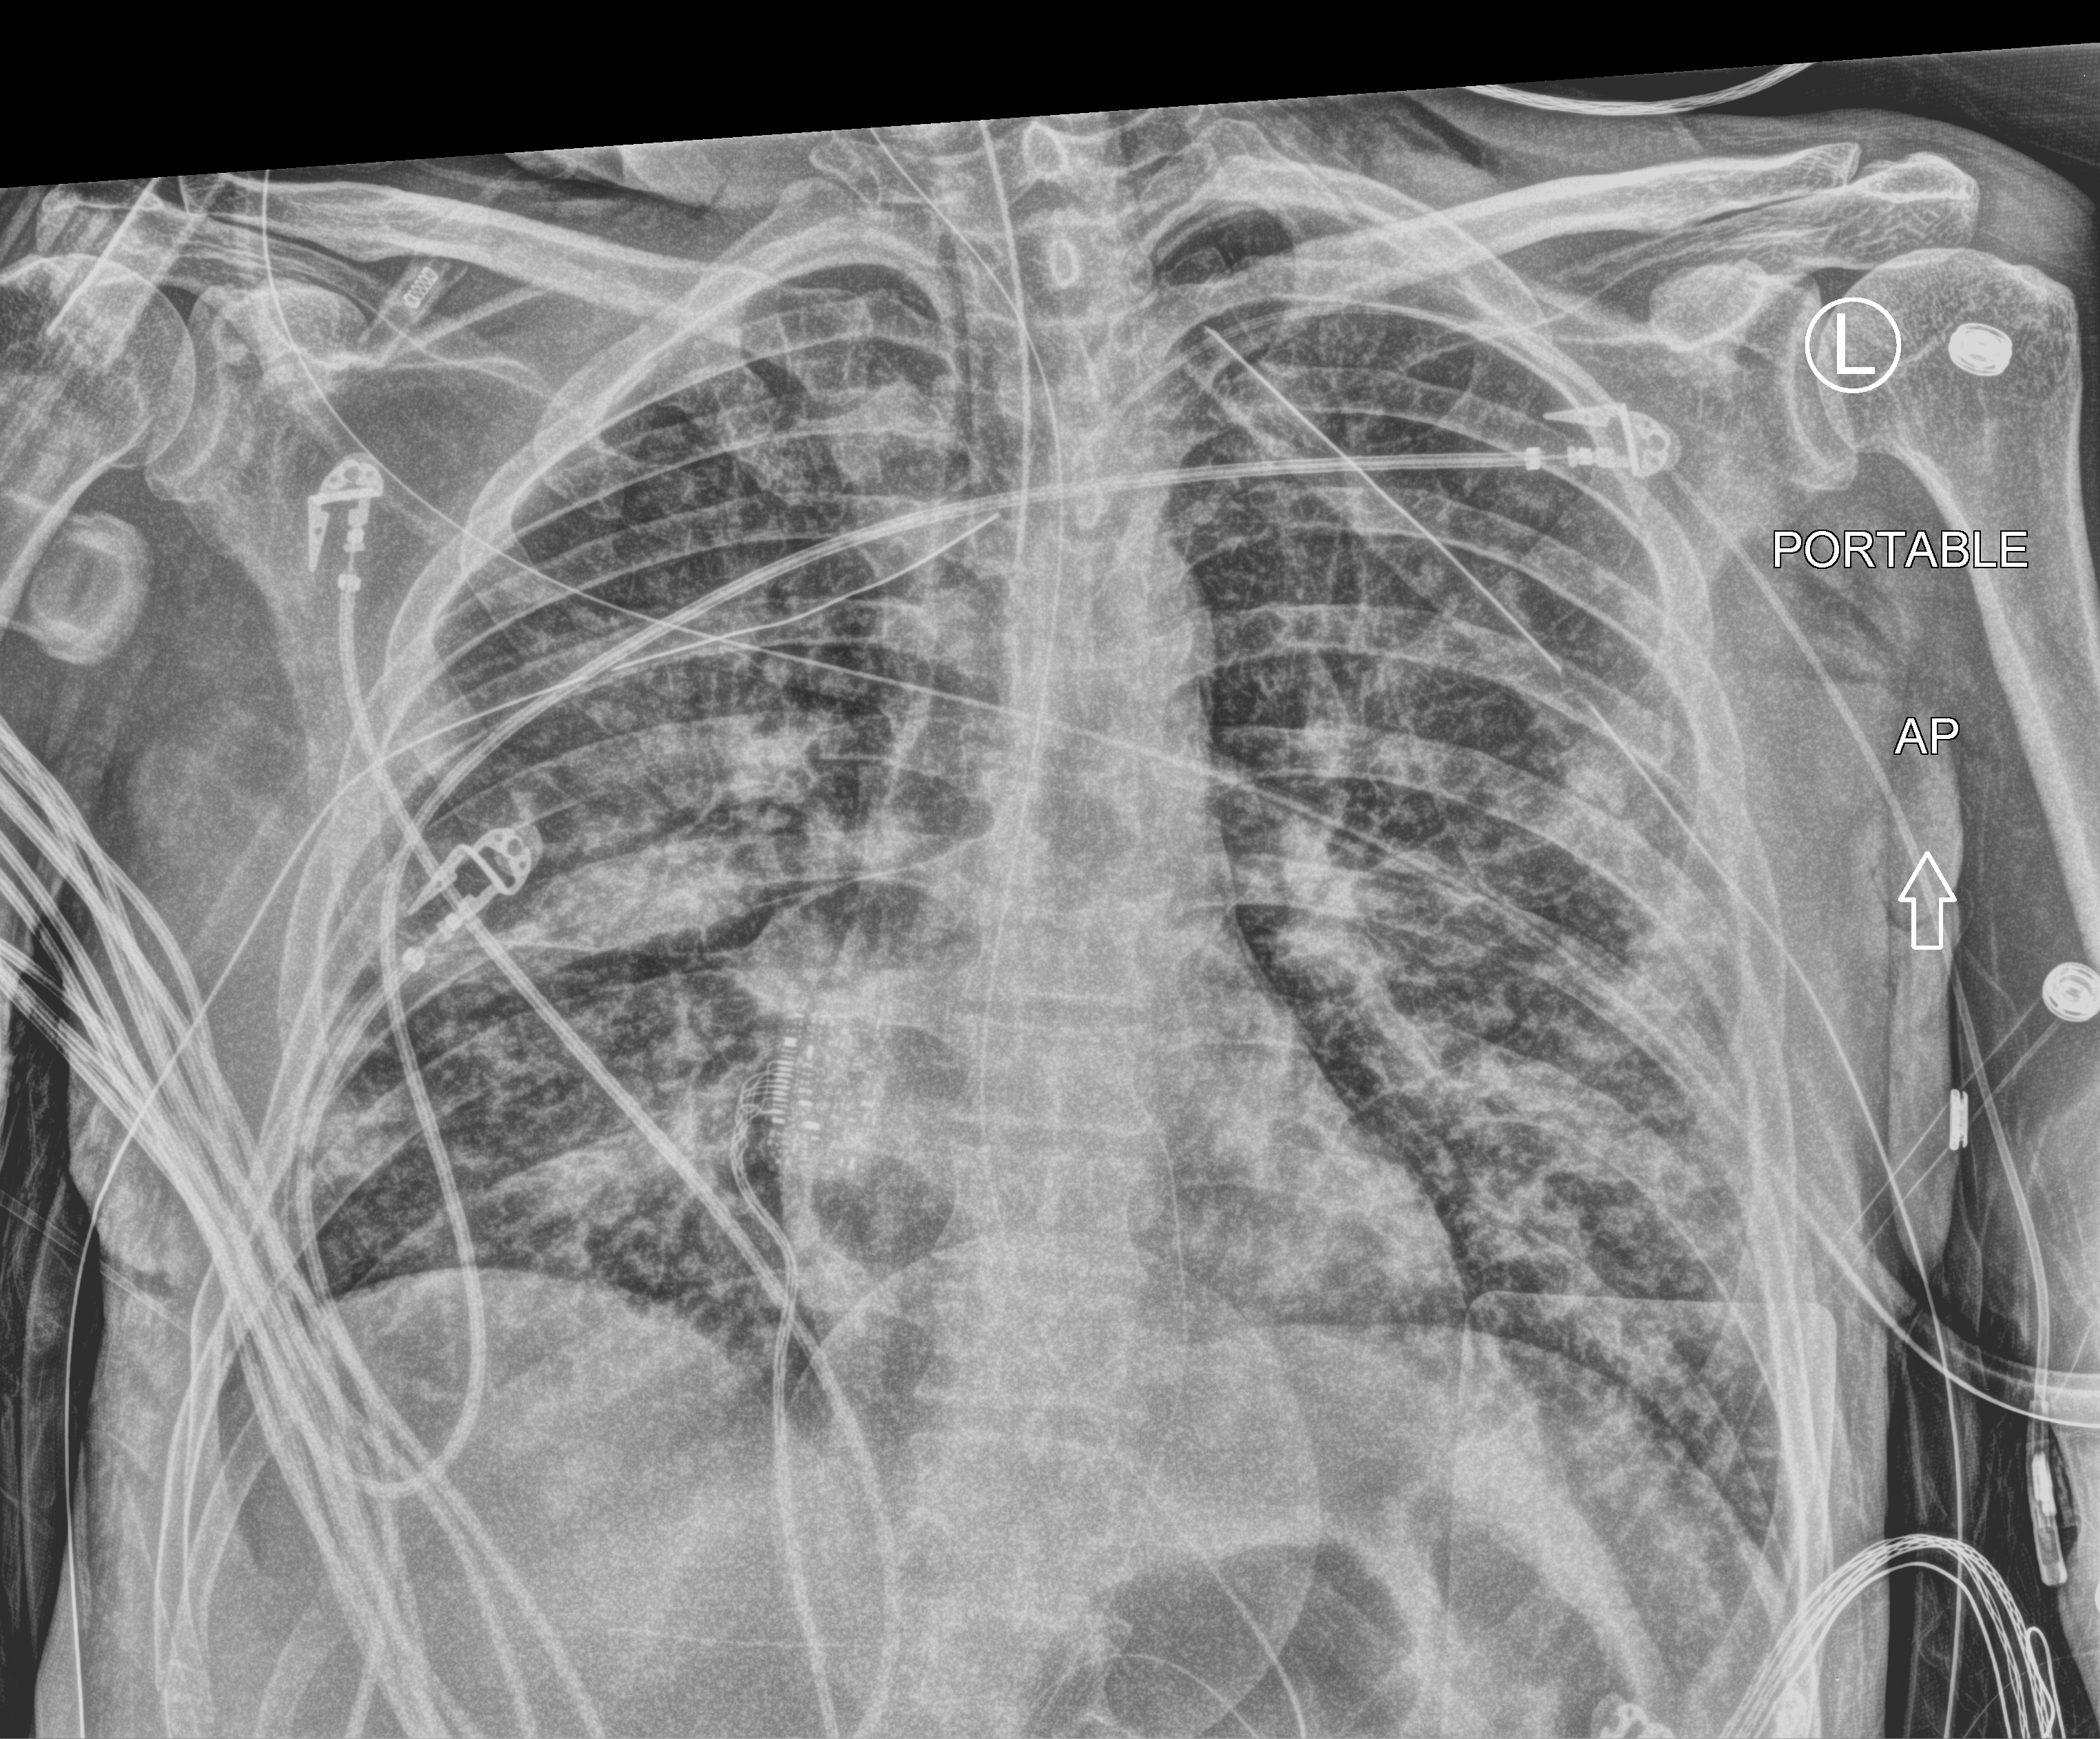
Chest X-ray (portable), anteroposterior (AP) projection. Male patient hospitalised with COVID-19, age 18–59 years.
Admission-level facts for this patient (not findings on this image; timing relative to this image not recorded): smoking status (admission record): never.